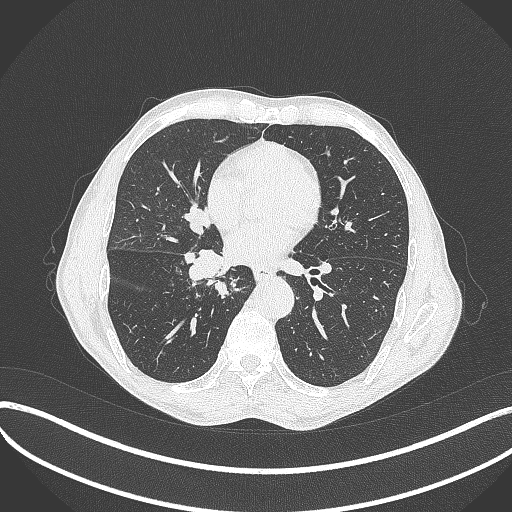
Chest CT, one axial slice; position 197 of 481 along the scan axis; reconstruction kernel B70f; 120 kVp; lung window (W 1500 / L -600 HU); 1 mm slice thickness; 512 × 512 image matrix, field of view 400 × 400 mm. Patient: male, 65 years. Case-level facts recorded for this patient, not image findings: clinical TNM (as recorded): T2a N0 M0.
Annotated regions visible in this slice (bounding box drawn by a radiologist):
- lung tumour (recorded histology: squamous cell carcinoma): bounding box (x1, y1, x2, y2) in pixels: (182, 249, 237, 296)